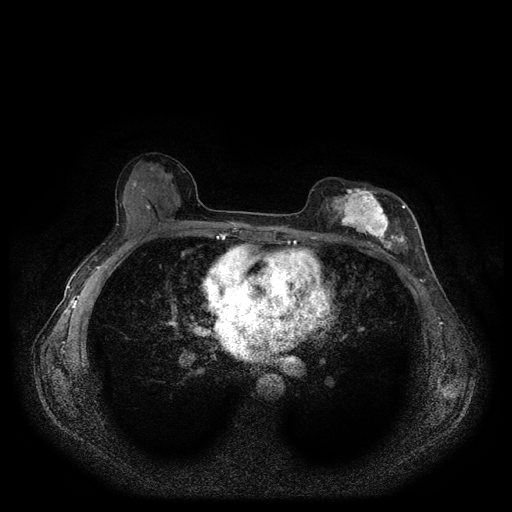
Breast MRI (dynamic contrast-enhanced, multi-phase), one axial slice. Position 56 of 116 along the scan axis. Dynamic contrast-enhanced series, time point 2 of 5 at this slice position (early post-contrast). 1.5 T. TE 2.6 ms, TR 5.3 ms. 512 × 512 image matrix, field of view 350 × 350 mm. Patient: female, 51 years.
Outlined on this slice (semi-automatic segmentation, software-assisted and operator-edited):
- breast lesion (labelled 'tumour' in the annotation; benign lesions carry a separate 'benign' label): bounding box <320,183,411,258> (left, top, right, bottom; pixels)